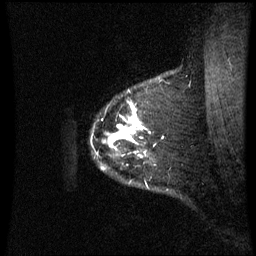
Breast MRI (dynamic contrast-enhanced), one sagittal slice. Dynamic contrast-enhanced series, image 2 of 3 at this slice position (ordered by acquisition). 1.5 T. TE 4.2 ms, TR 8.9 ms. 2.4 mm slice thickness. 256 × 256 image matrix. Patient: female, 42 years. From the clinical record (not read from this slice): setting: breast cancer imaged before/during neoadjuvant chemotherapy; receptor status: HER2-positive.
Annotated regions visible in this slice (semi-automatic segmentation, software-assisted and operator-edited):
- analysis volume of interest (the breast-tissue region the enhancement analysis was run in; not a lesion): bounding box <103,103,165,168> (left, top, right, bottom; pixels)
- tumour enhancement mask (voxels above the 70 % enhancement threshold inside the analysis volume of interest): <115,113,145,140>